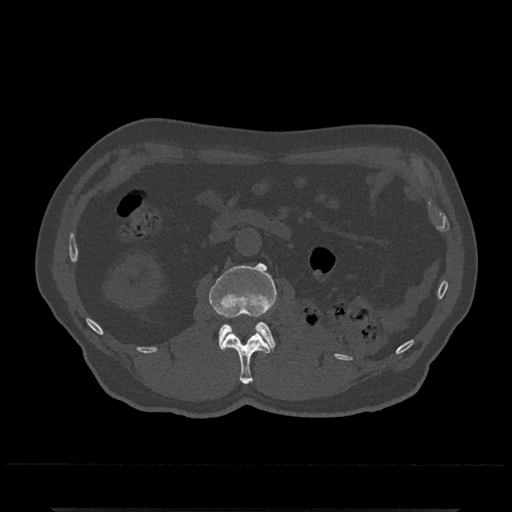
CT including the spine, one axial slice. Position 324 of 797 along the scan axis. Reconstruction kernel Br40s/3. 120 kVp. Bone window (W 1800 / L 400 HU). 512 × 512 image matrix. Male patient, age 67 years. Case-level facts recorded for this patient, not image findings: primary cancer: prostate.
Outlined on this slice (semi-automatically segmented with operator editing):
- L1 vertebra: bounding box [x1, y1, x2, y2] px = [220, 331, 270, 385]
- L2 vertebra: [210, 263, 278, 352]